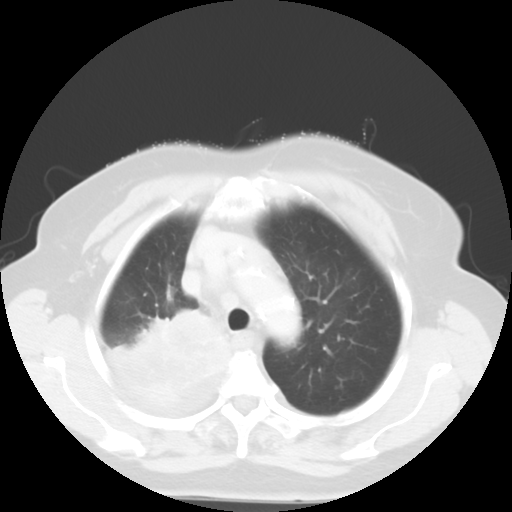
Chest CT, one axial slice. Reconstruction kernel STANDARD. 120 kVp. Lung window (W 1500 / L -600 HU). 5 mm slice thickness. 512 × 512 image matrix, field of view 333 × 333 mm. Female patient, age 81 years. Case-level facts recorded for this patient, not image findings: clinical TNM (as recorded): T4 N3 M1b.
Annotated regions visible in this slice (bounding box drawn by a radiologist):
- lung tumour (recorded histology: adenocarcinoma): bounding box <94,305,233,409> (left, top, right, bottom; pixels)